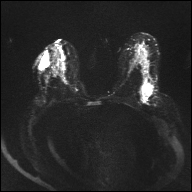
Breast MRI, one axial slice; position 18 of 32 along the scan axis; diffusion-weighted series; image 2 of 4 stored at this slice position (different b-values; order by instance number); 1.5 T; 4 mm slice thickness; 192 × 192 image matrix, field of view 360 × 360 mm. Female patient.
Annotated regions visible in this slice (outlined manually by an expert reader):
- tumour on diffusion-weighted imaging: bounding box [x1, y1, x2, y2] px = [142, 85, 153, 95]